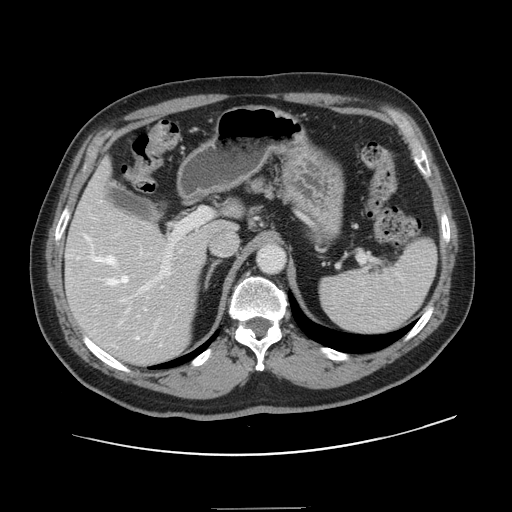
Contrast-enhanced abdominal CT, one axial slice; position 91 of 143 along the scan axis; intravenous contrast given; soft-tissue window (W 400 / L 40 HU); 2.5 mm slice thickness; 512 × 512 image matrix, field of view 402 × 402 mm. Male patient, age 62 years. From the clinical record (not read from this slice): diagnosis: colorectal cancer liver metastases, imaged before liver resection; multiple liver metastases: yes.
Outlined on this slice (manually delineated by an expert):
- hepatic veins: bounding box [x1, y1, x2, y2] px = [85, 235, 161, 346]
- liver: [66, 166, 237, 363]
- planned liver remnant (the part of the liver to remain after resection): [68, 166, 237, 248]
- portal vein (with intrahepatic branches): [77, 208, 211, 317]